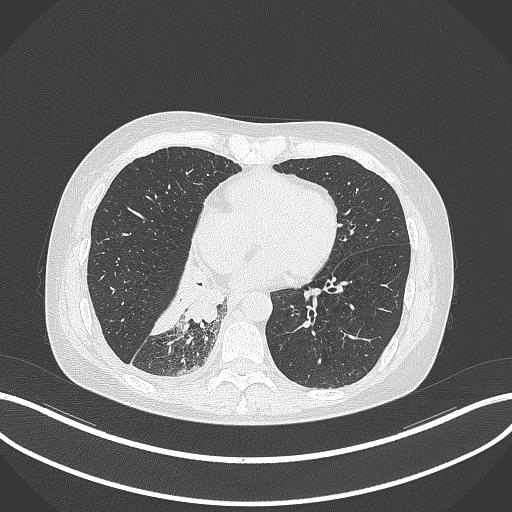
Chest CT, one axial slice; position 112 of 329 along the scan axis; 120 kVp; lung window (W 1500 / L -600 HU); 1 mm slice thickness; 512 × 512 image matrix, field of view 400 × 400 mm. Patient: female, 63 years. From the clinical record (not read from this slice): clinical TNM (as recorded): T1c N0 M0.
Structures marked on this image (bounding box drawn by a radiologist):
- lung tumour (recorded histology: adenocarcinoma): bounding box [x1, y1, x2, y2] px = [177, 261, 228, 322]